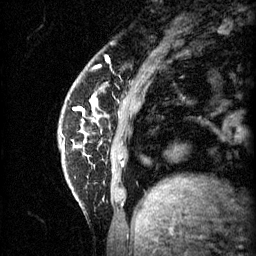
Breast MRI (dynamic contrast-enhanced), one sagittal slice. Position 9 of 60 along the scan axis. 3 images stored at this slice position (order not interpretable as contrast timing). 1.5 T. TE 4.2 ms, TR 11 ms. 2 mm slice thickness. 256 × 256 image matrix, field of view 180 × 180 mm. Patient: female, 62 years.
Annotated regions visible in this slice (semi-automatically segmented with operator editing):
- analysis volume of interest (the breast-tissue region the enhancement analysis was run in; not a lesion): box from (x=60, y=84) to (x=97, y=133) px
- tumour enhancement mask (voxels above the 70 % enhancement threshold inside the analysis volume of interest): (x=84, y=100)–(x=95, y=113)